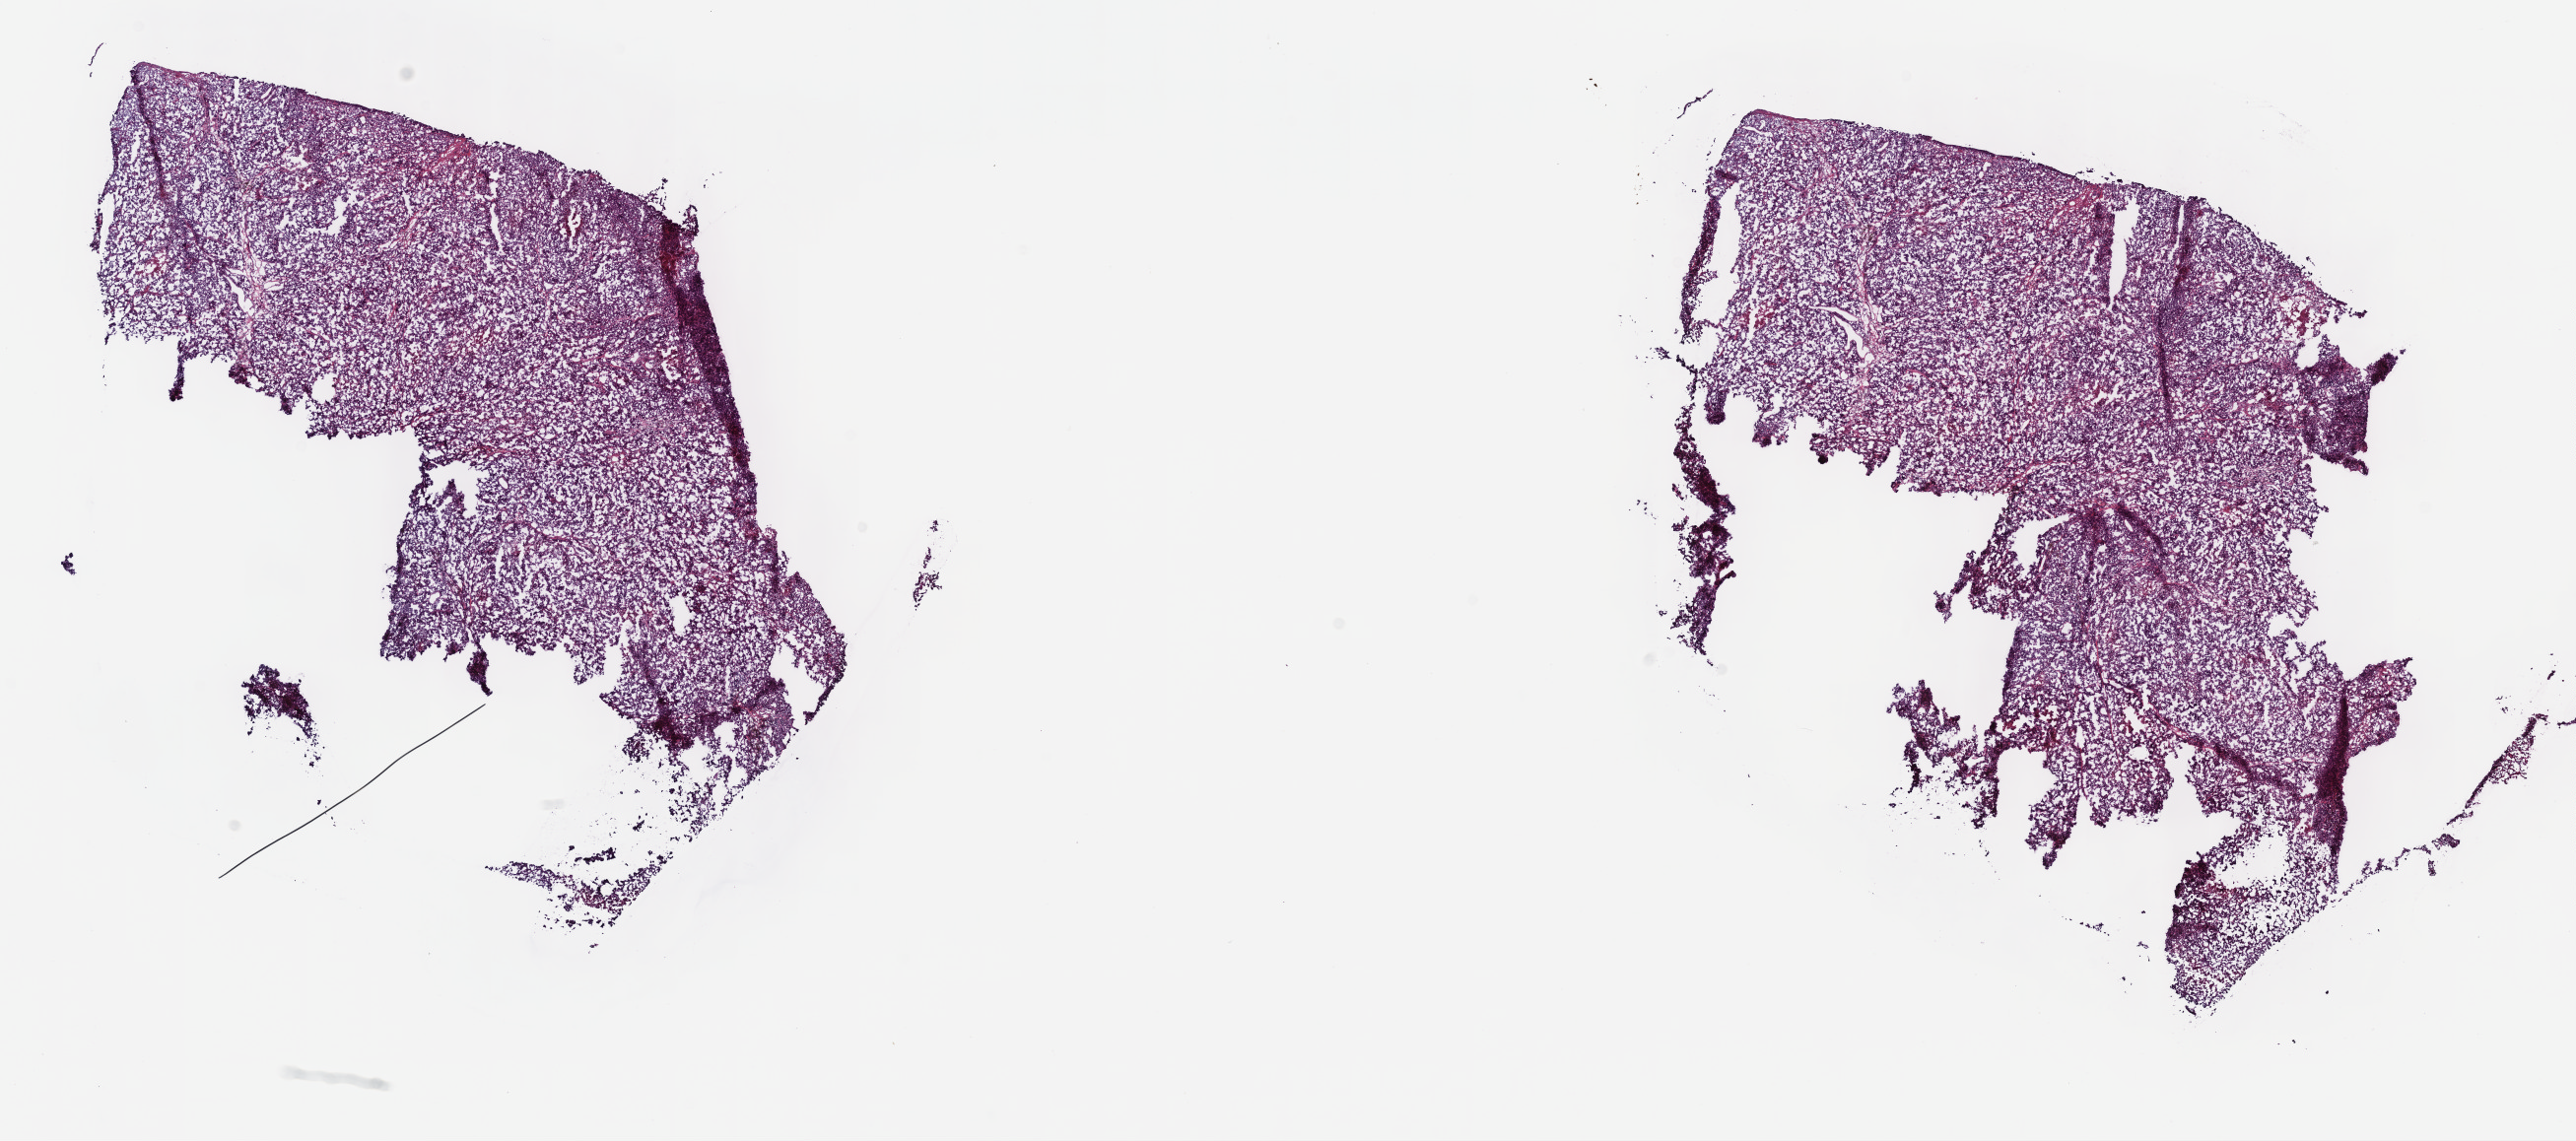
Digitized Hematoxylin and eosin (H&E) stained tissue section (whole slide), whole scanned area (about 21.1 x 9.4 mm, from a 40x scan) shown as a low-resolution overview, frozen section, metastatic tumour sample, sampled site: connective, subcutaneous and other soft tissues of pelvis. Male, age 45 years at initial diagnosis. Pathologist review of this section (percent, as recorded): tumour cells 100%, tumour nuclei 95%, normal cells 0%, stromal cells 0%, necrosis 0%. Infiltration values recorded for this section: lymphocyte infiltration 0%, monocyte infiltration 0%, neutrophil infiltration 0%.
• this section: metastatic tumour tissue
• patient diagnosis: Malignant melanoma, NOS